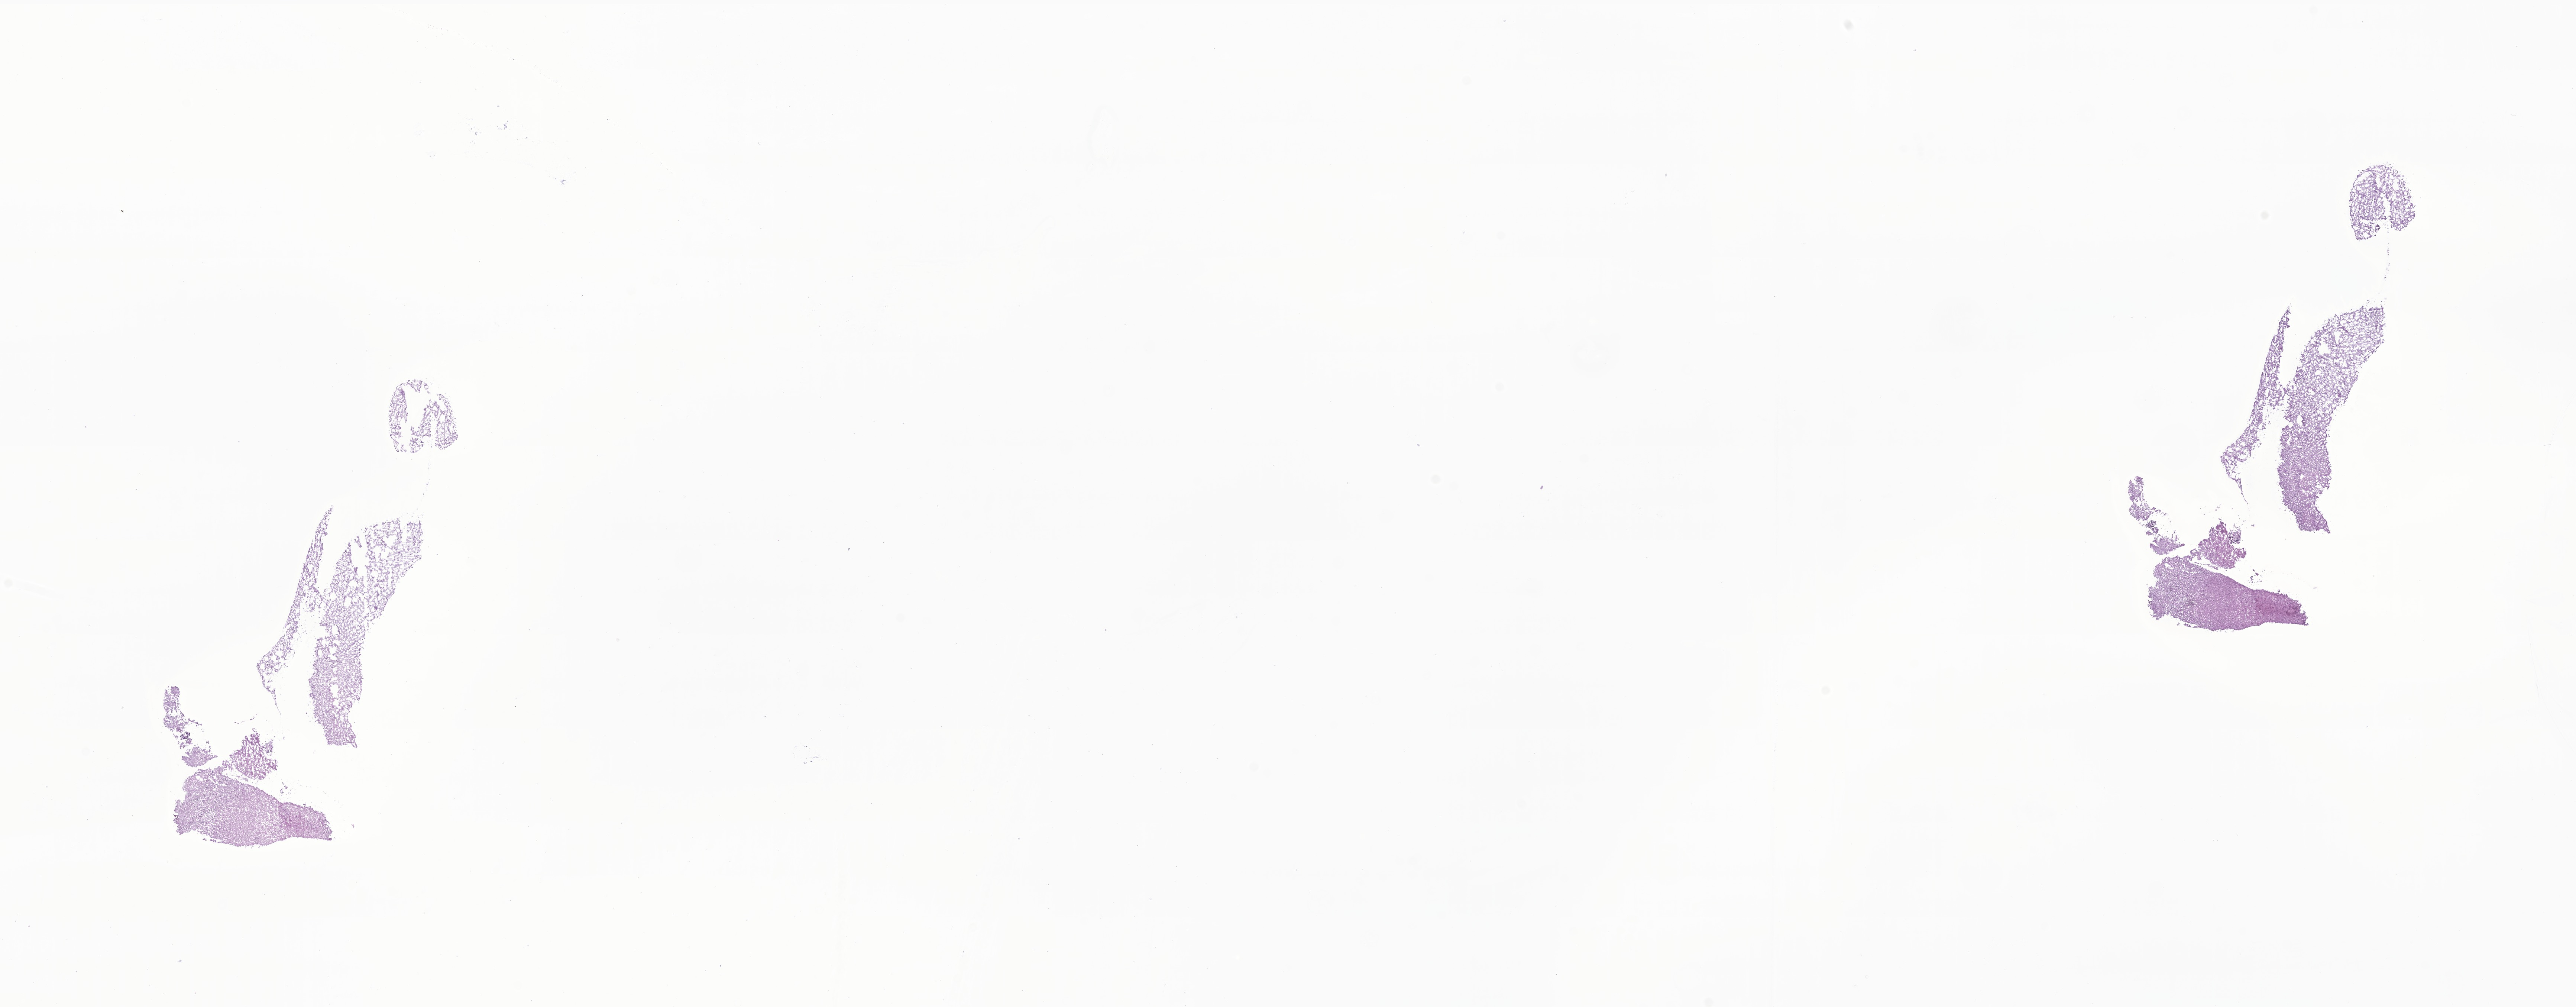
Digitized hematoxylin and eosin (H&E)-stained section of tumor tissue from the cerebellum, a low-resolution overview of the entire scanned area, about 29.2 x 11.4 mm; frozen section. Female patient, age 753 days (about 2.1 years).
Diagnosis (ICD-O-3 morphology term): Neoplasm, uncertain whether benign or malignant.